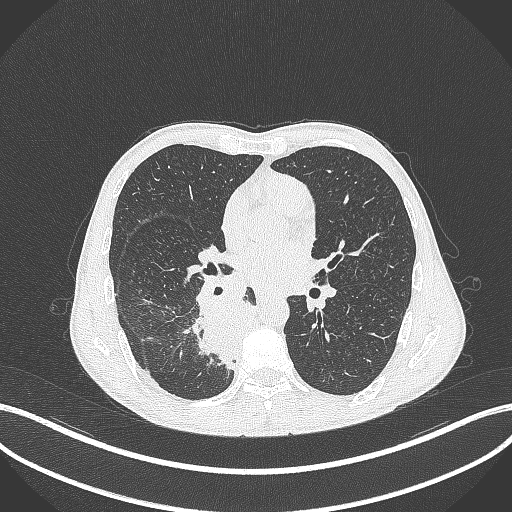
Chest CT, one axial slice. Position 189 of 371 along the scan axis. Reconstruction kernel B70f. Lung window (W 1500 / L -600 HU). 1 mm slice thickness. 512 × 512 image matrix, field of view 400 × 400 mm. Patient: male, 58 years. From the clinical record (not read from this slice): clinical TNM (as recorded): T3 N1 M1.
Structures marked on this image (rectangle marked by the reading radiologist):
- lung tumour (recorded histology: squamous cell carcinoma): bounding box (x1, y1, x2, y2) in pixels: (184, 292, 255, 371)